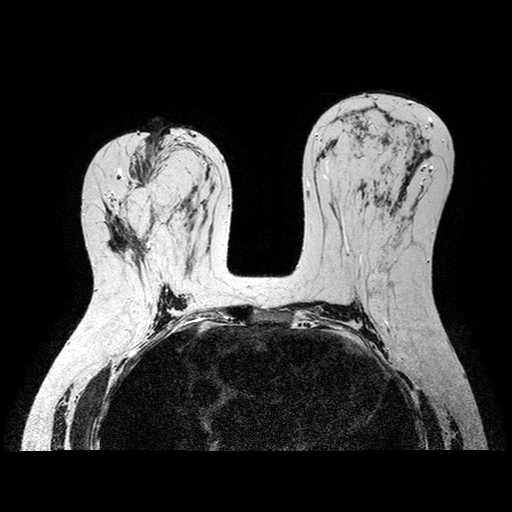
Breast MRI examination; 2 images, each one mid-volume slice chosen by position.
Image 1: axial T2-weighted / STIR image, series "T2W_TSE SENSE", slice 43 of 84.
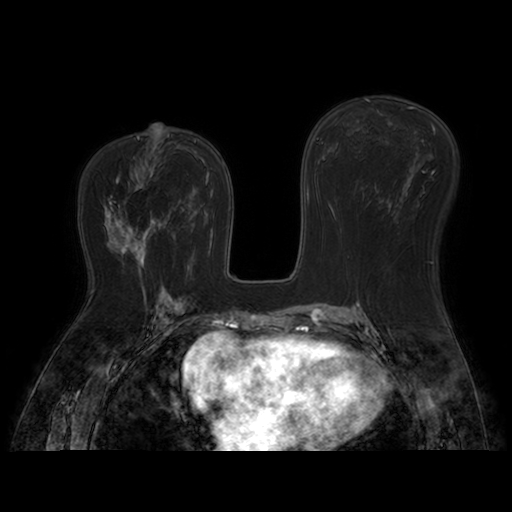
Image 2: post-contrast dynamic axial slice, series "AX BLISS_AUTO SENSE", slice 43 of 84, dynamic phase 5 of 8.
Radiologist's MRI impression, right breast: Right Breast: There is moderate background enhancement. The first mass in the upper, outer, posterior quadrant now measures 1.8 x 1.2 cm (previously 2.1 x 1.7 cm) and the second mass which is anterior and medial to the first now measures 1.4 x 0.7 (previously 1.4 x 1.0 cm). The enlarged intramammary lymph node in the upper, outer posterior quadrant has also slightly decreased in size now measuring 0.8 x 0.9 cm (previously 1.1 x 1.6 cm). The right axillary lymph node has decreased in size and now measures 0.8 x 0.8 cm (previously 1.2 x 0.9 cm). There is no skin thickening or nipple inversion present.
Patient-level pathology facts (from the clinical record, not from the images): pathology diagnosis: invasive lobular (right breast); receptor status (as recorded): ER pos, PR pos, HER2 neg; Ki-67 (as recorded): low prolif; pathology report notes: Invasive Lobular Carcinoma, S/P Neoadjuvant Therapy Size of invasive component: 2.5X2X2cm (largest focus) Tumor focality: Multiple foci of invasion Number of lymph nodes with macrometastases (>0.2 cm): 2 Size of largest metastatic deposit: 1.3cm Extranodal extension: Present.